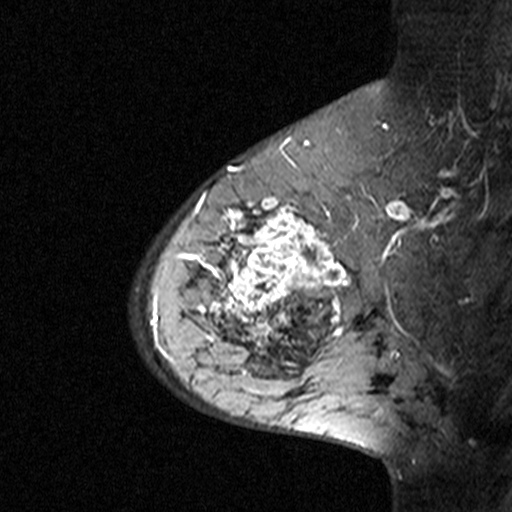
Breast MRI (dynamic contrast-enhanced), one sagittal slice. Position 29 of 44 along the scan axis. Dynamic contrast-enhanced study with each time point stored as its own series, time point 3 of 4 at this slice position (ordered by acquisition time). 1.5 T. TE 4.5 ms, TR 11 ms. 3 mm slice thickness. 512 × 512 image matrix. Female patient, age 65 years. From the clinical record (not read from this slice): setting: breast cancer imaged before/during neoadjuvant chemotherapy; receptor status: HER2-positive.
Outlined on this slice (semi-automatically segmented with operator editing):
- analysis volume of interest (the breast-tissue region the enhancement analysis was run in; not a lesion): bounding box (x1, y1, x2, y2) in pixels: (182, 190, 353, 361)
- tumour enhancement mask (voxels above the 90 % enhancement threshold inside the analysis volume of interest): (182, 190, 352, 354)